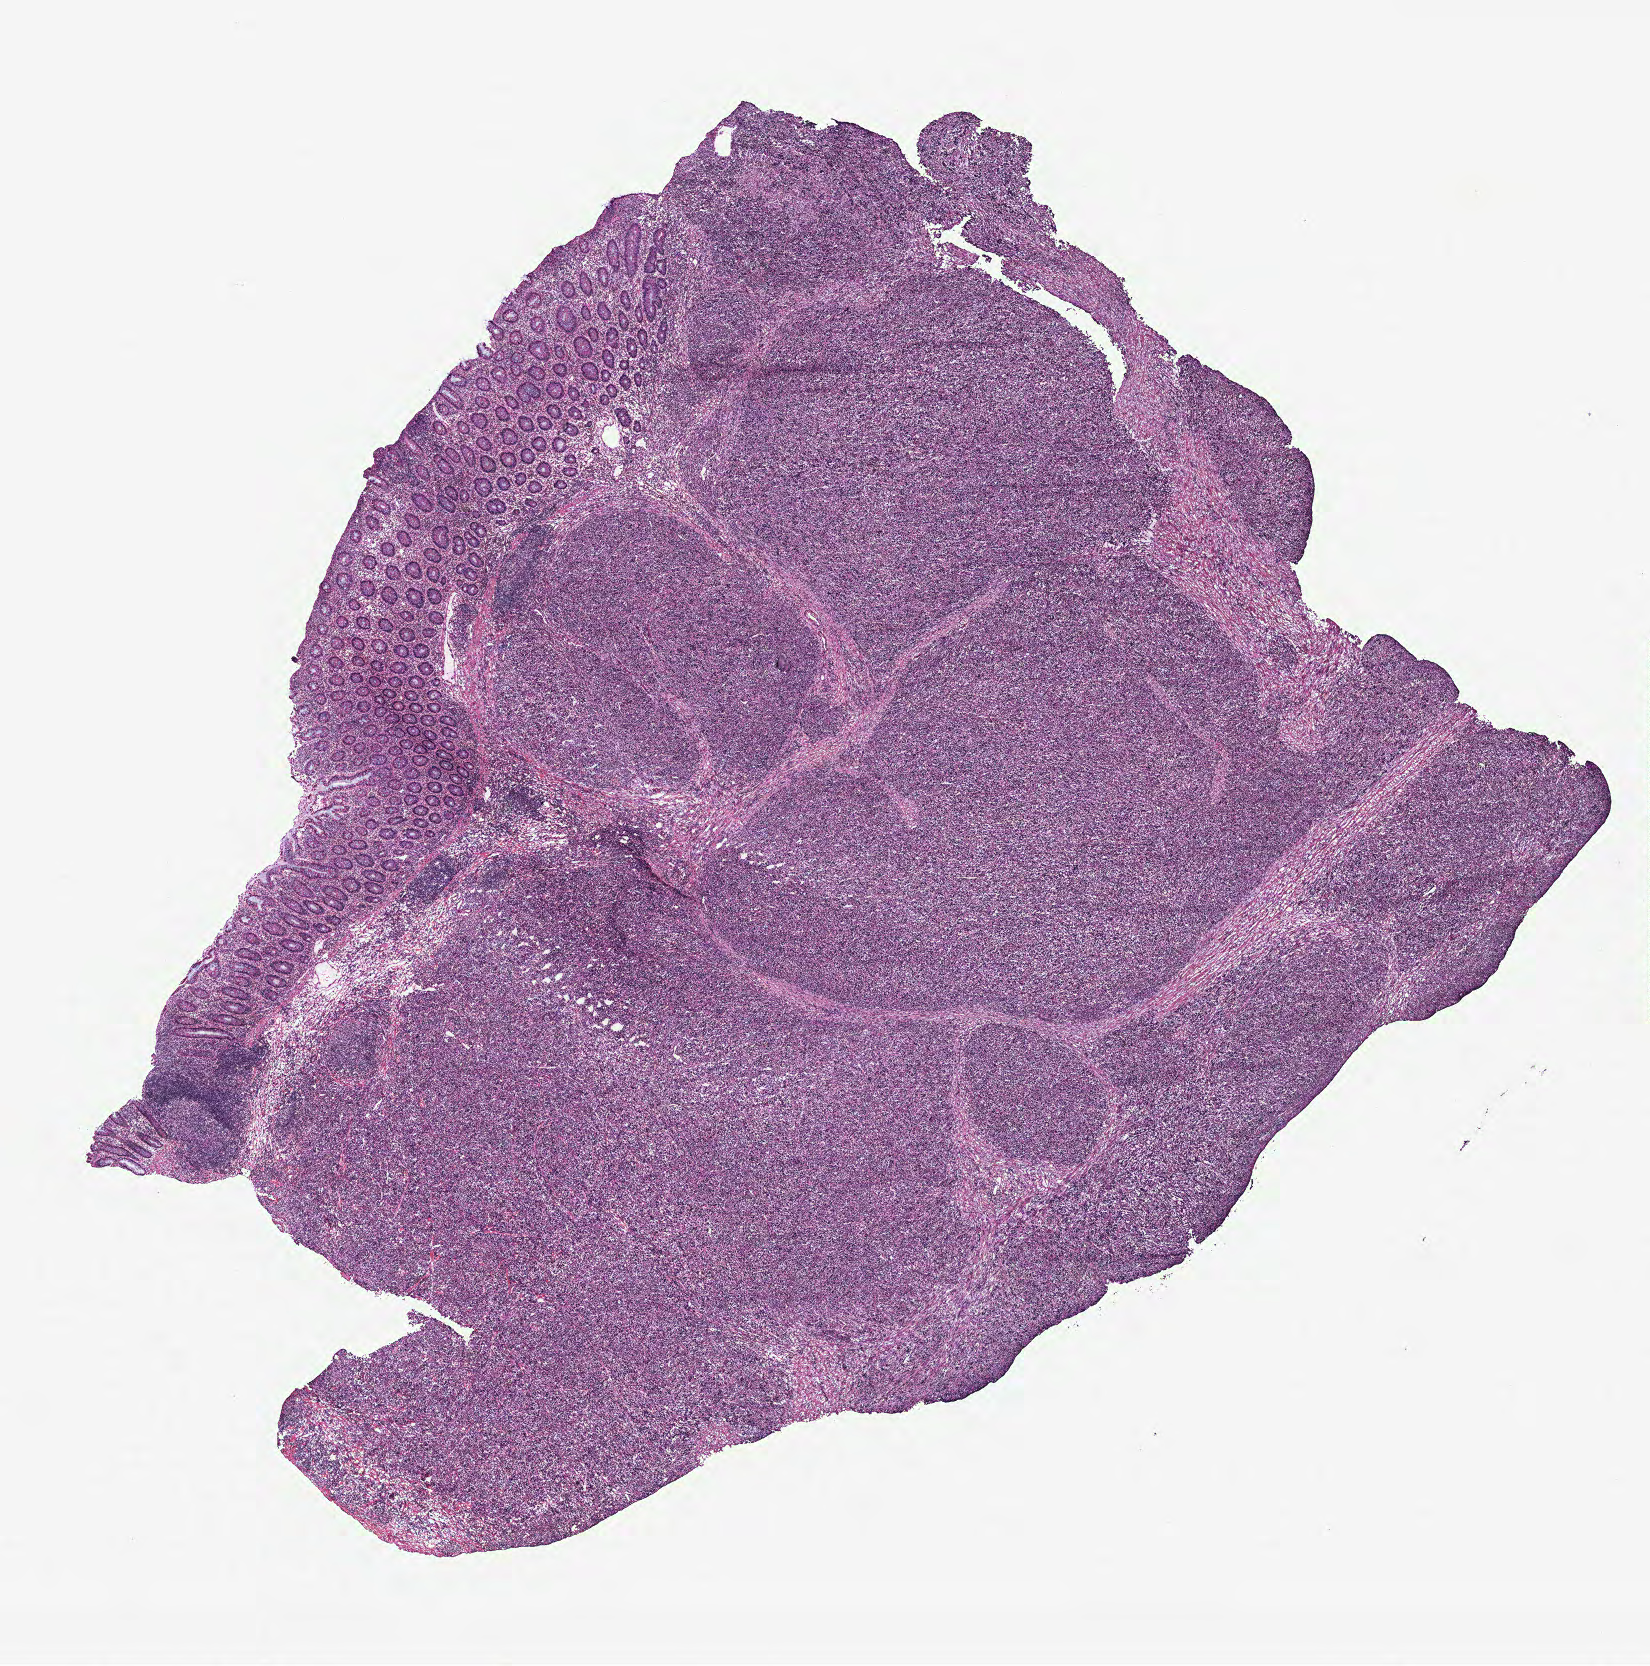
Digitized H&E-stained tissue section (whole slide), a low-resolution overview of the entire scanned area, about 13.2 x 13.3 mm (acquisition: 40x scan). Colon, tissue type not recorded.
Patient diagnosis (cohort enrolment): colon cancer (colon).